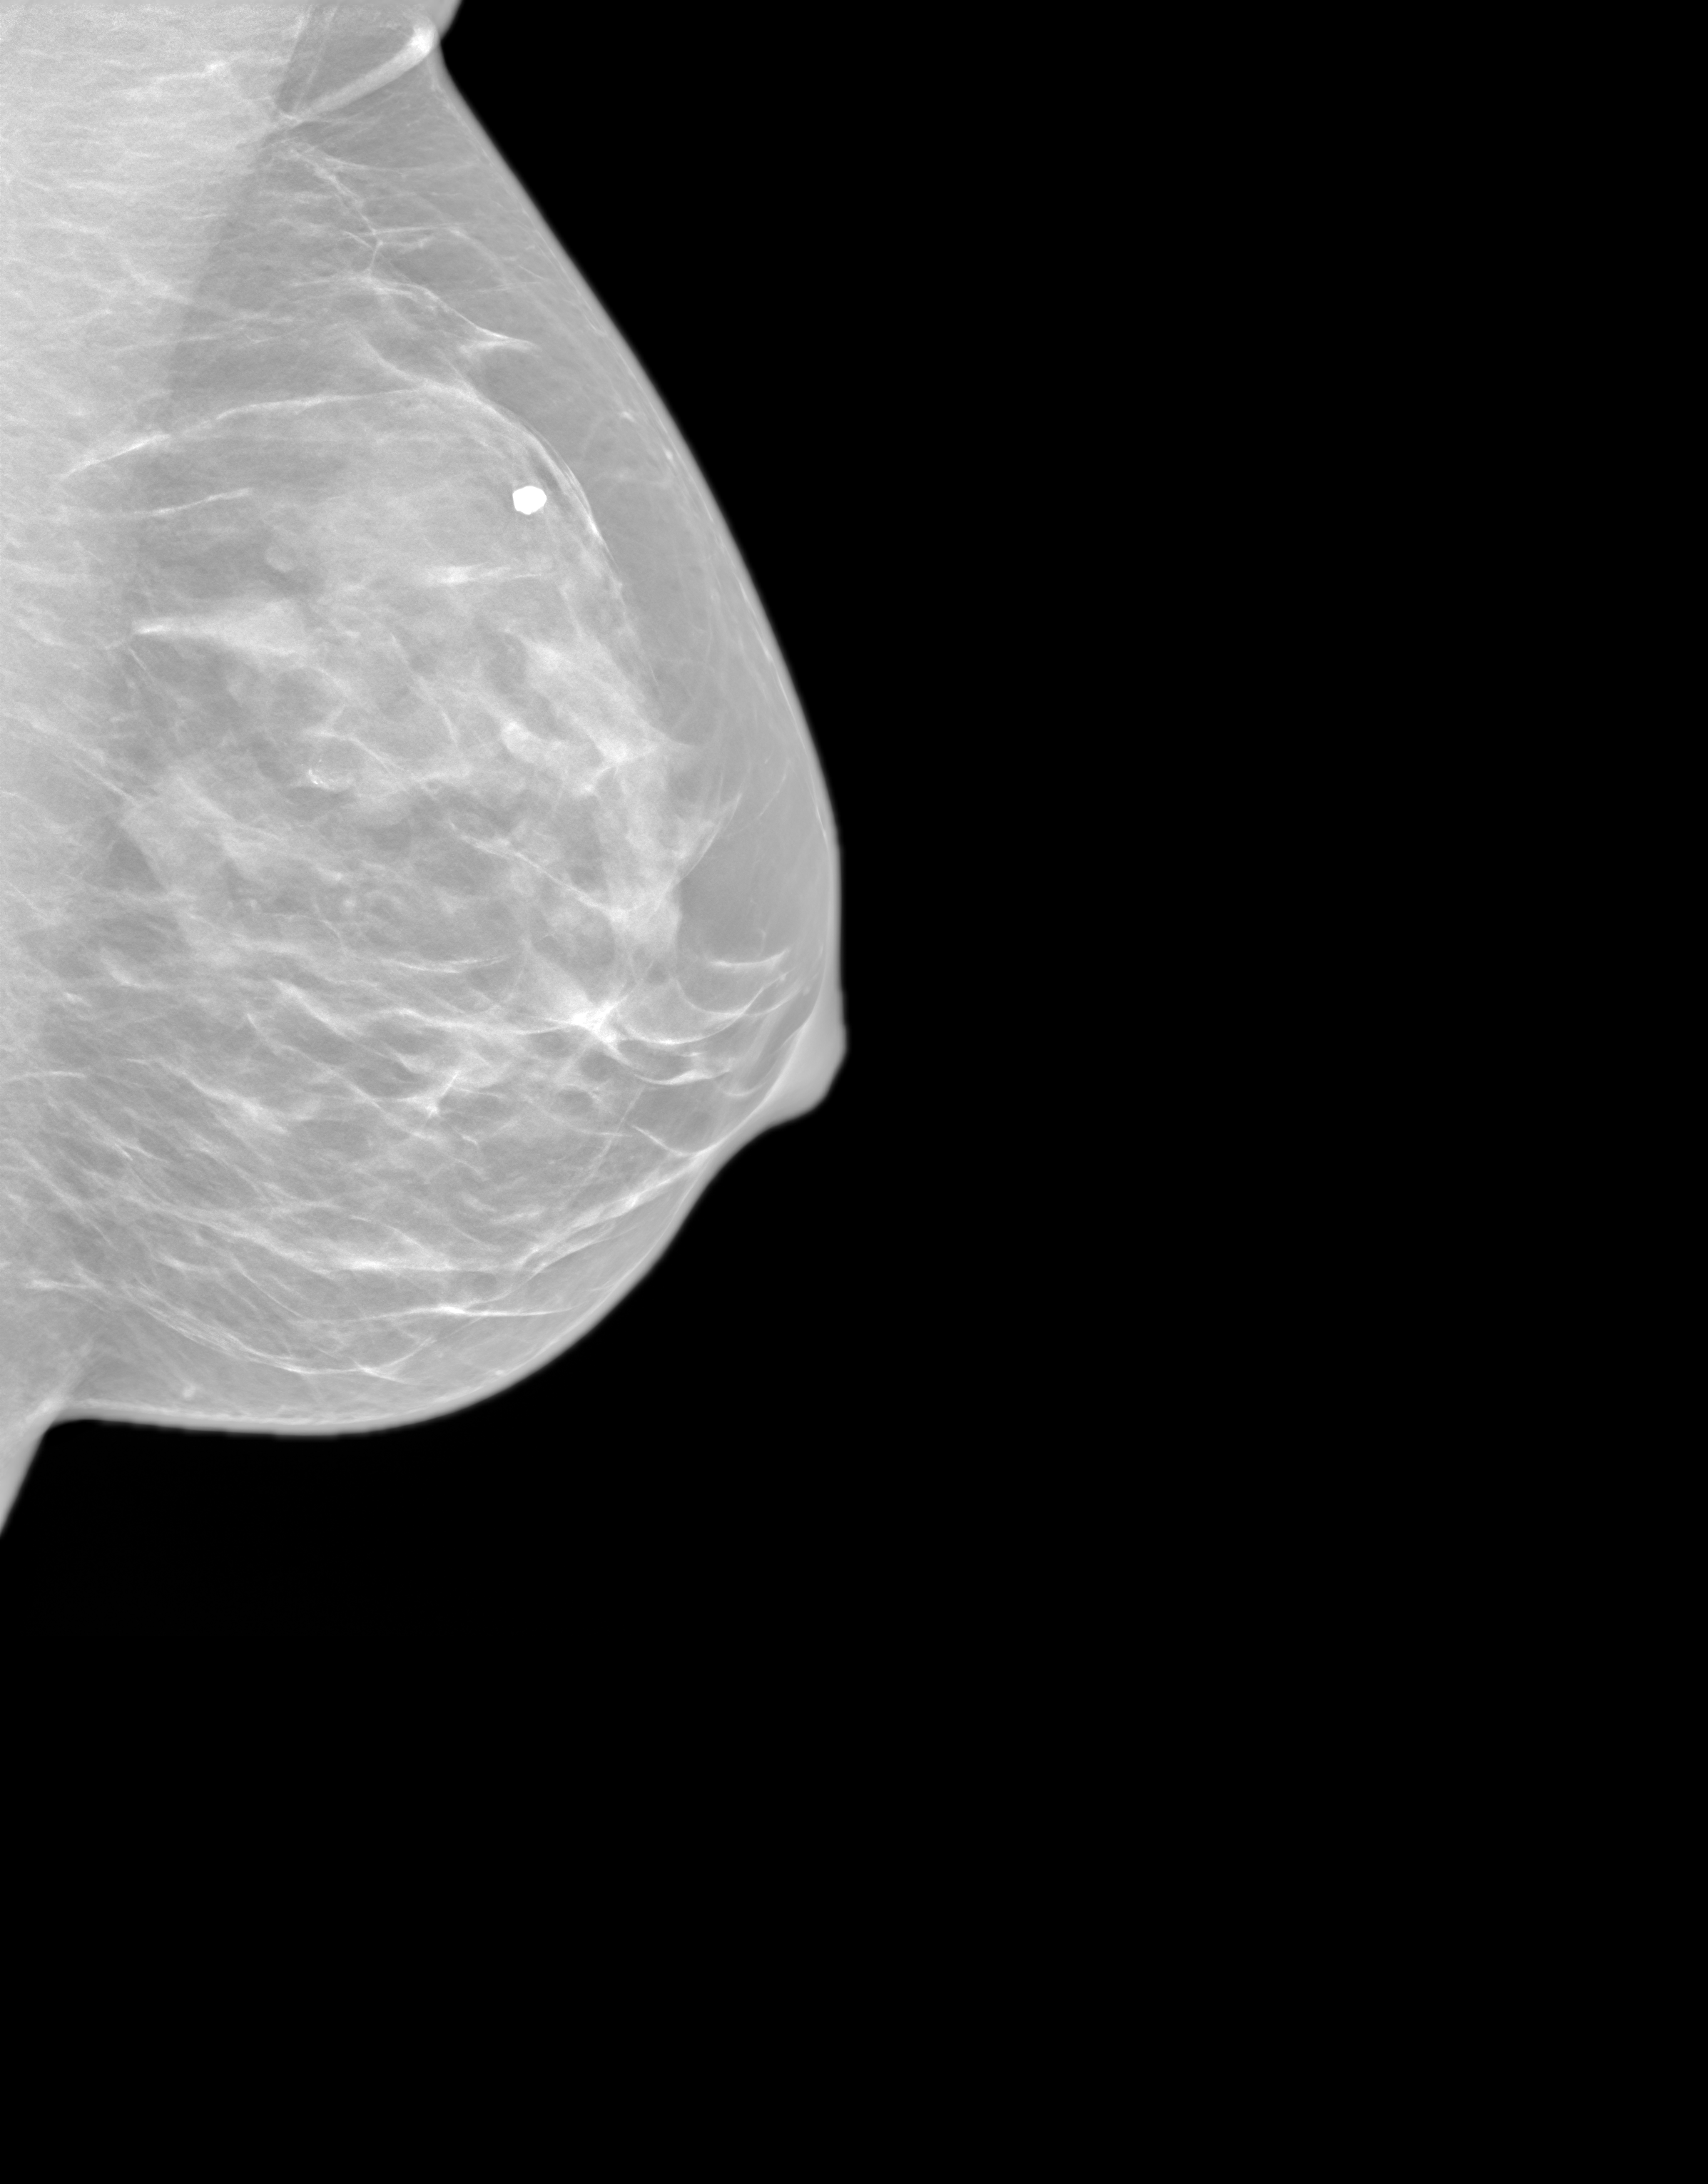
Synthesized 2-D mammogram reconstructed from digital breast tomosynthesis; left breast; medio-lateral oblique projection; screening examination. Patient: female, 51 years.
- breast density at the screening exam (both breasts): heterogeneously dense (BI-RADS density category c)
- final BI-RADS category for the screening round (tomosynthesis exam, both breasts): category 2
- recall: no recall after this screen